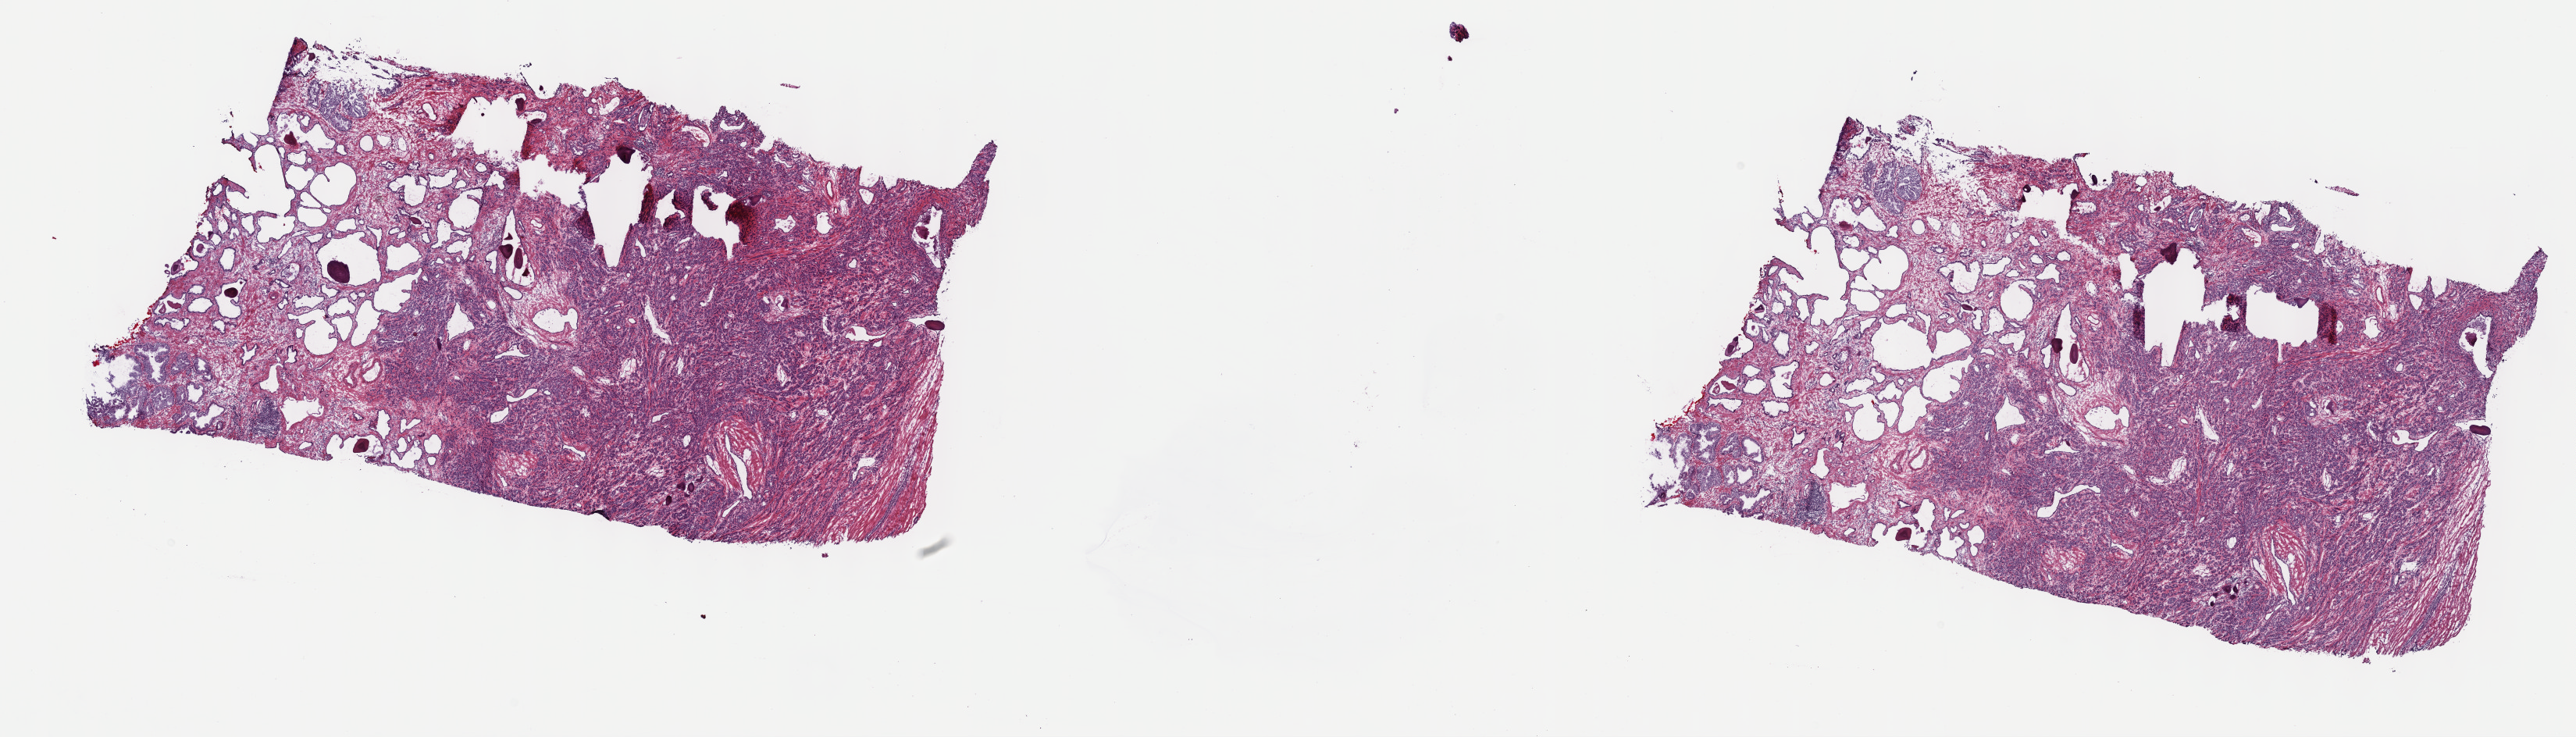
Whole-slide histology image, H&E-stained — shown as a low-resolution overview of the whole scanned area (about 26.7 x 7.6 mm, slide scanned at 40x). Frozen section from the top of the tissue portion. Primary tumour sample from the prostate. Patient: male, age at initial diagnosis 68 years. Gleason score: 9 (4+5). Composition of this section per pathologist review: tumour cells 60%, tumour nuclei 75%, normal cells 35%, stromal cells 5%, necrosis 0%. Infiltration values recorded for this section: lymphocyte infiltration 0%, monocyte infiltration 0%, neutrophil infiltration 0%.
Diagnosis: Adenocarcinoma, NOS. Laterality: bilateral. Lymph nodes positive (case pathology): 1 of 11 examined.